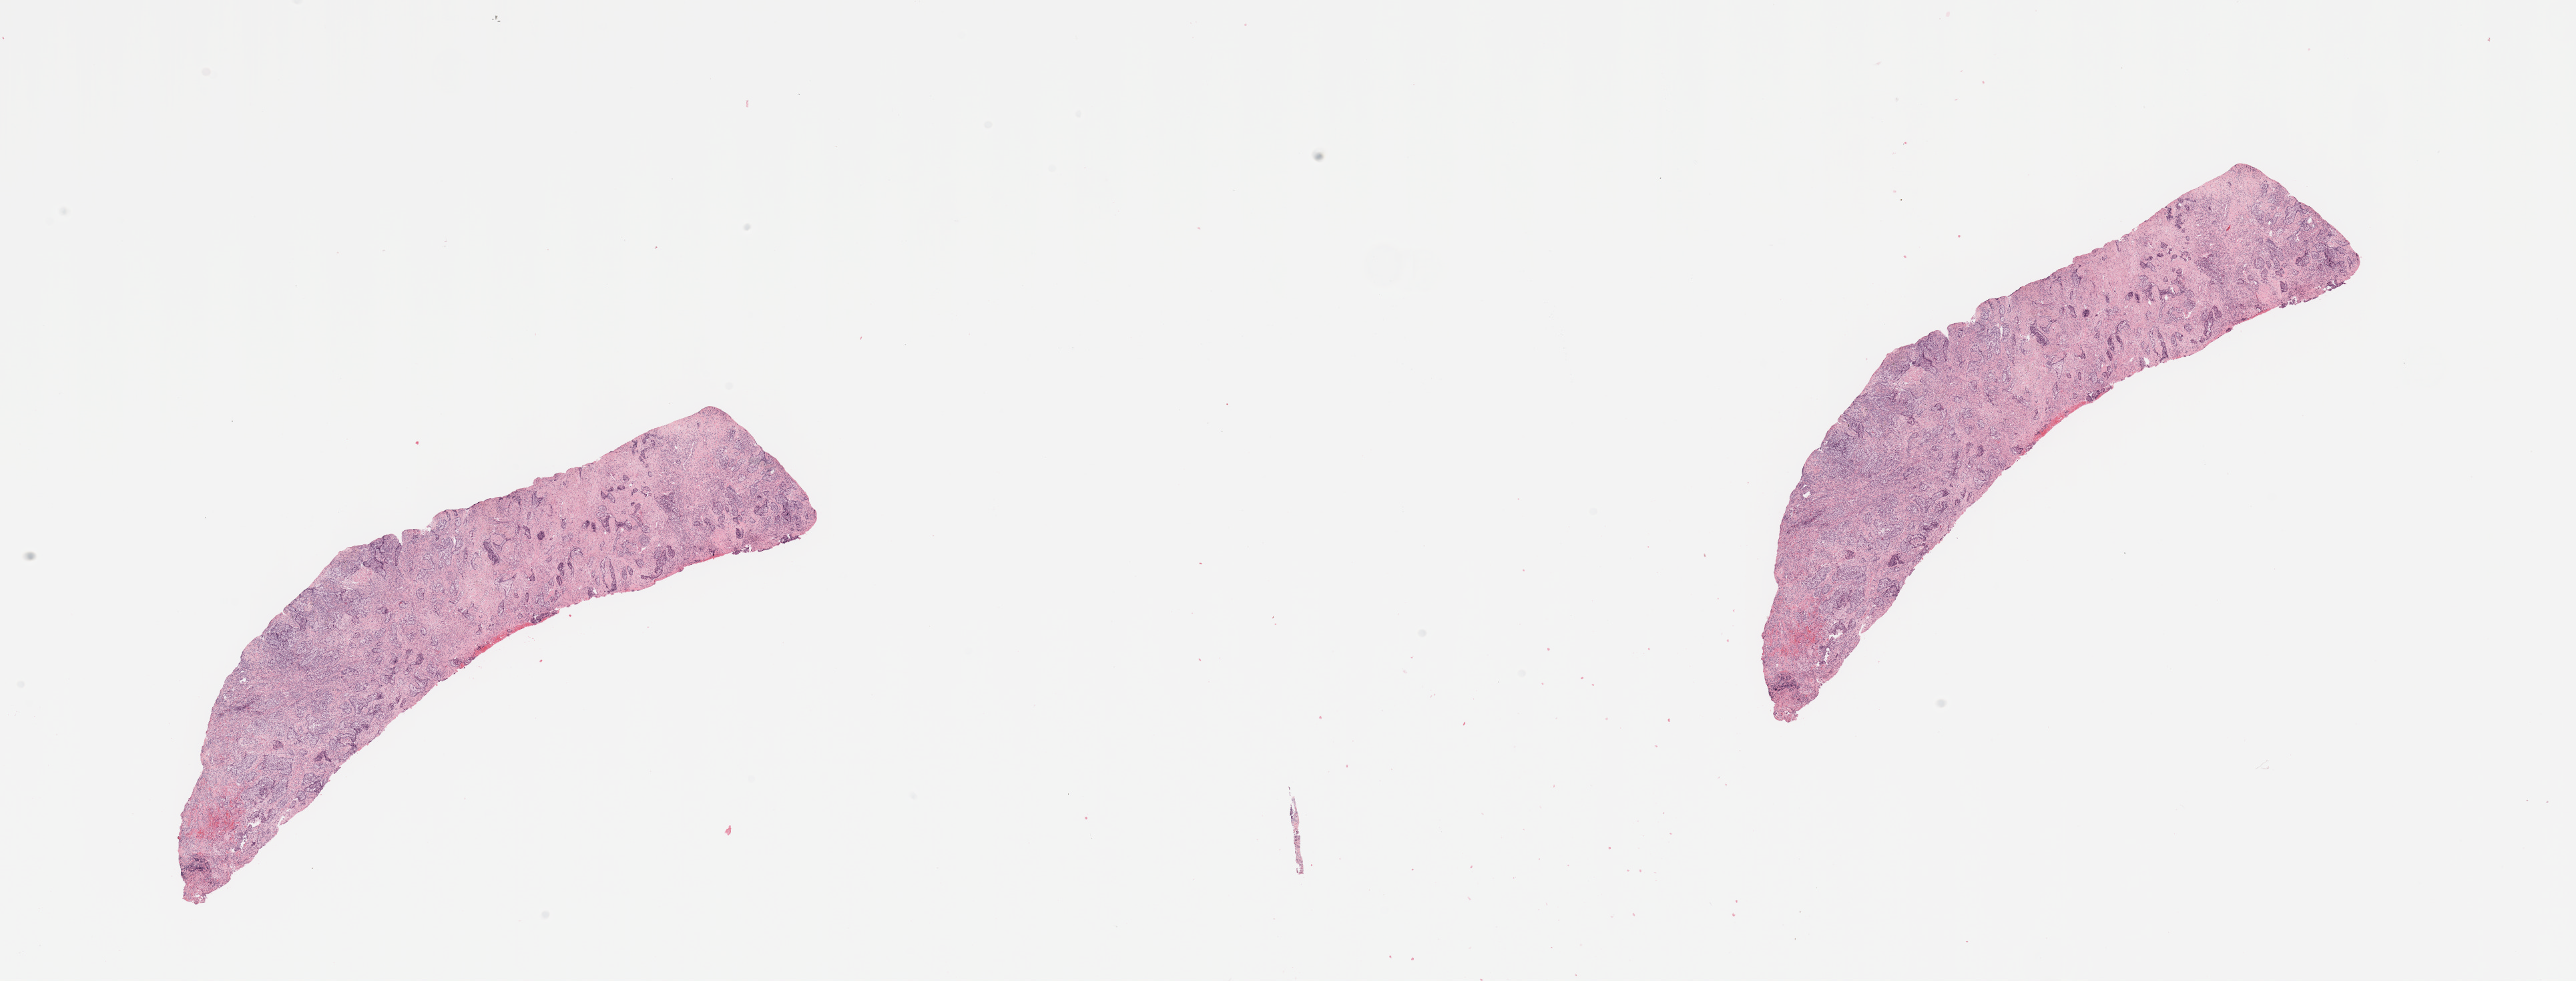
Hematoxylin and eosin (H&E) stained whole-slide image — whole scanned area (about 30.5 x 11.6 mm) shown as a low-resolution overview. Tumour tissue sample, sampled site: lung. 71-year-old male patient. Histologic grade: G2 (moderately differentiated). Composition of this section per pathologist review: tumour nuclei 60%, necrosis 5%.
AJCC pathologic stage: IA. Primary tumour site (as recorded): left upper lobe. Diagnosis: Adenocarcinoma, NOS.